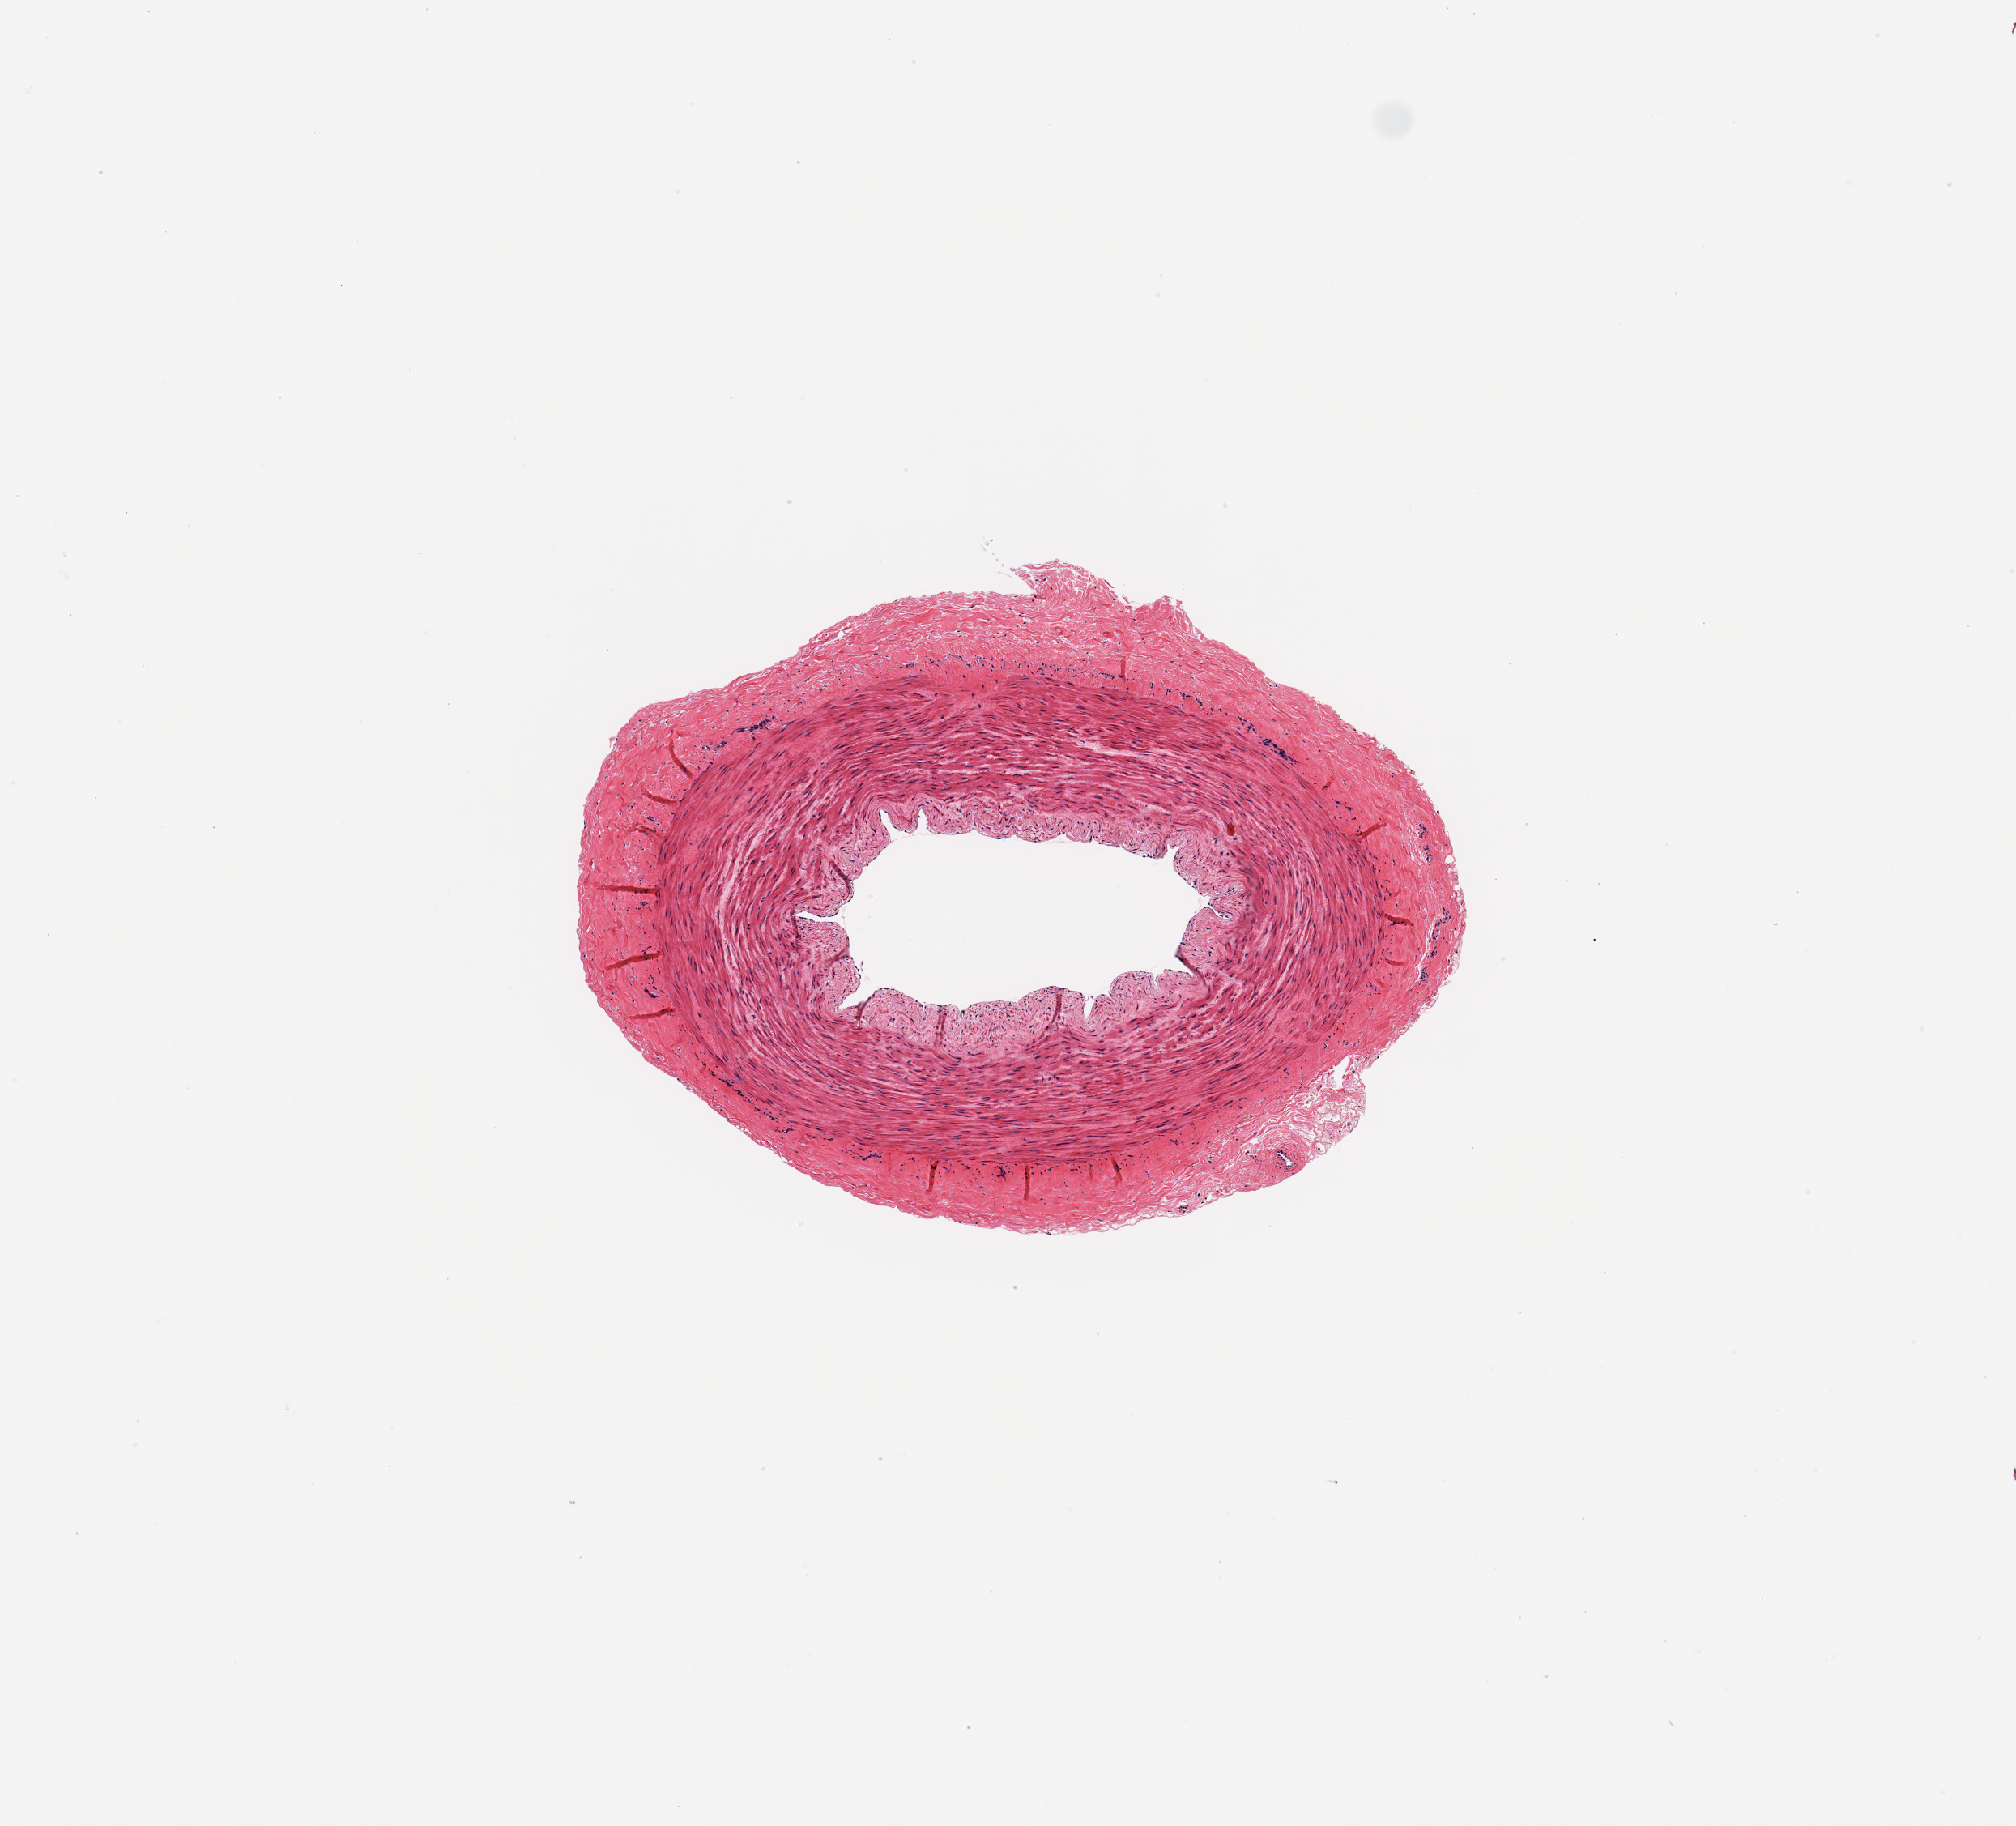
Hematoxylin and eosin (H&E) whole-slide image, a low-resolution overview of the entire scanned area, about 4.9 x 4.5 mm; PAXgene-fixed paraffin-embedded (PFPE) section; sampled site (target tissue): tibial artery; donor tissue sample. Donor: female.
• pathologist's review note for this sample: 1 piece; no lesions; well trimmed